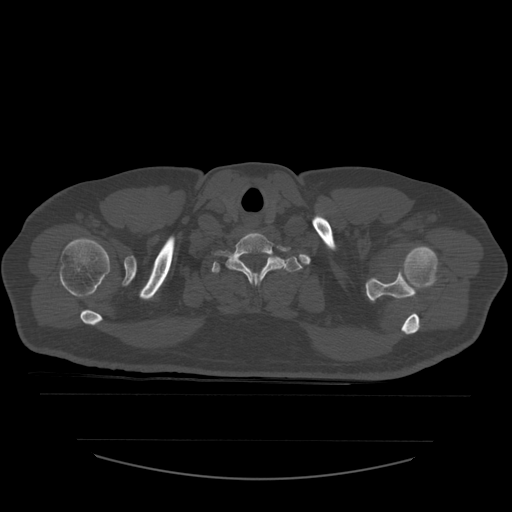
CT including the spine, one axial slice. Slice 478 of 532 in the series (ordered by position). Reconstruction kernel STANDARD. 120 kVp. Bone window (W 1800 / L 400 HU). 1.25 mm slice thickness. 512 × 512 image matrix. Patient age 44 years. Case-level facts recorded for this patient, not image findings: primary cancer: soft tissue sarcoma.
Structures marked on this image (semi-automatic segmentation, software-assisted and operator-edited):
- T1 vertebra: bounding box <212,257,303,273> (left, top, right, bottom; pixels)